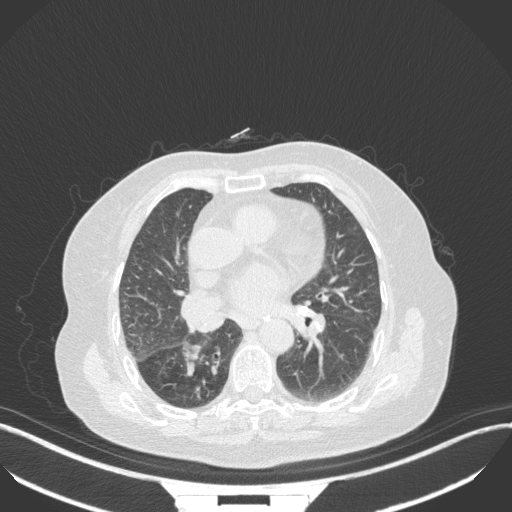
Chest CT, one axial slice. Slice 155 of 329 in the series (ordered by position). 120 kVp. Lung window (W 1500 / L -600 HU). 1 mm slice thickness. 512 × 512 image matrix, field of view 400 × 400 mm. Female patient, age 75 years. From the clinical record (not read from this slice): clinical TNM (as recorded): T1b N0 M1a; histopathological grade: G1.
Structures marked on this image (bounding box drawn by a radiologist):
- lung tumour (recorded histology: squamous cell carcinoma): box from (x=182, y=341) to (x=206, y=364) px